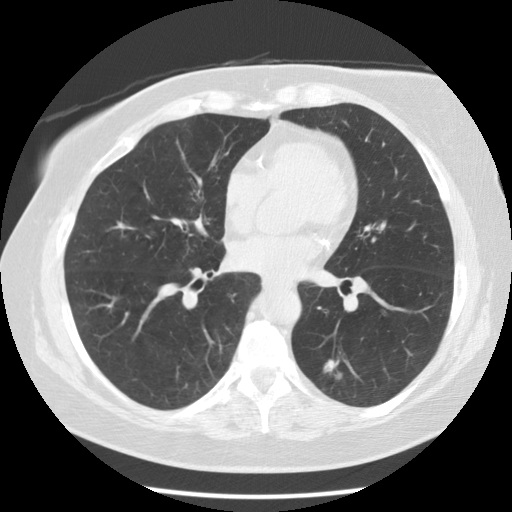
Axial slice from a low-dose chest CT screening exam, second screening round (one year after baseline), lung window (W 1500 / L -600 HU), standard (soft-tissue) reconstruction kernel (STANDARD), slice 64 of 118 in the series, 512 × 512 image matrix. Female participant, aged 59 years at enrolment. Current smoker at enrolment.
- Expert reader's lesion annotation, bounding box <298,341,367,407> (left, top, right, bottom; pixels).
- The screening reader recorded 5 non-calcified nodules or masses ≥4 mm on this exam (right upper lobe, right lower lobe, right lower lobe, left lower lobe, left lower lobe); which of them this box marks is not recorded.
- Official screen result: positive, other.
- Participant outcome: lung cancer diagnosed 343 days after this screen (after the third annual screen) — adenocarcinoma, NOS, left lower lobe, poorly differentiated (G3), stage IA (AJCC 6th edition), 15 mm at pathology.